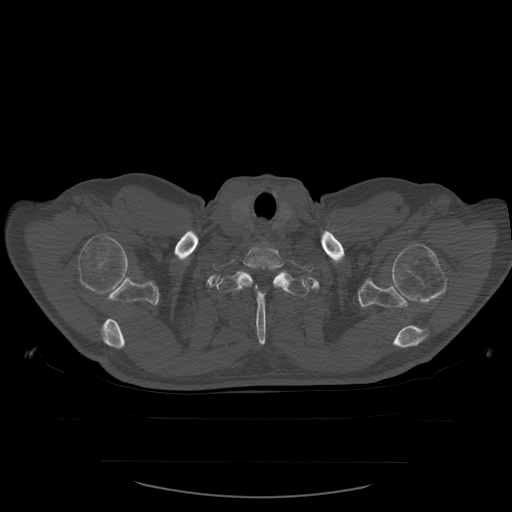
CT including the spine, one axial slice. Position 482 of 590 along the scan axis. Bone window (W 1800 / L 400 HU). 1.25 mm slice thickness. 512 × 512 image matrix, field of view 479 × 479 mm. Patient age 71 years. Case-level facts recorded for this patient, not image findings: primary cancer: lung.
Structures marked on this image (semi-automatically segmented with operator editing):
- T1 vertebra: bounding box [x1, y1, x2, y2] px = [213, 246, 314, 292]
- T2 vertebra: [216, 271, 312, 345]